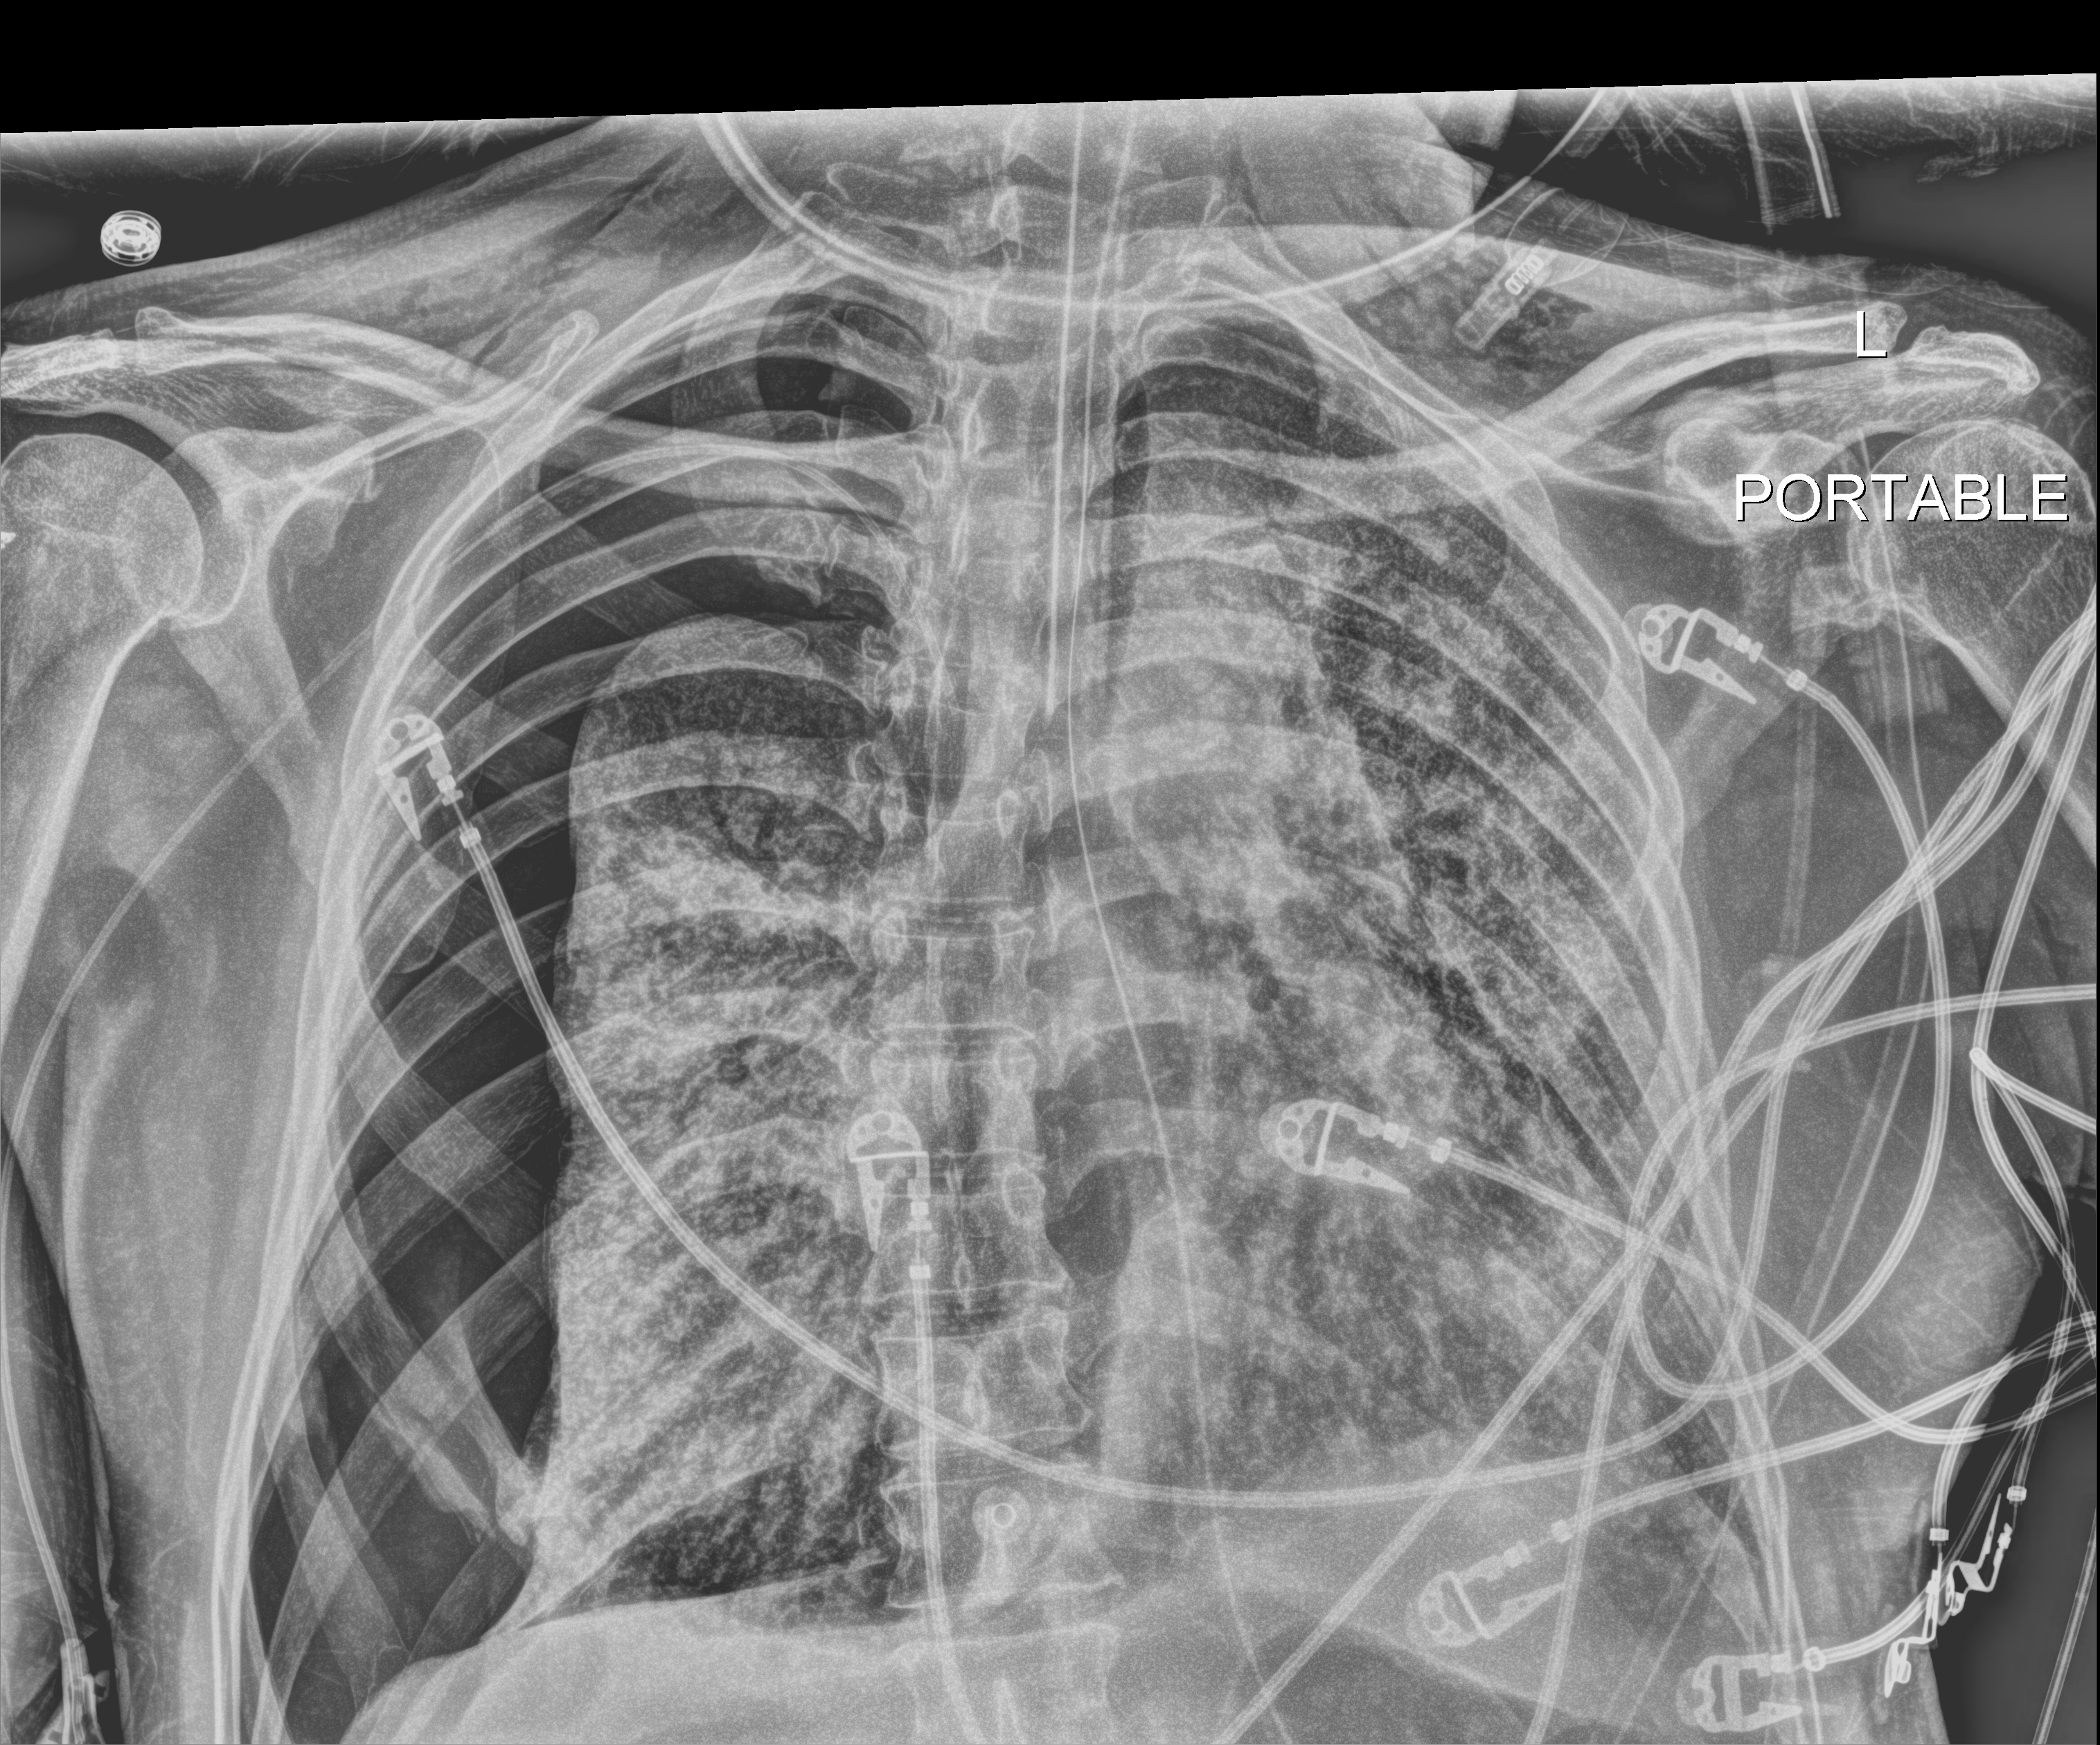
Chest X-ray (portable). Male patient hospitalised with COVID-19, age 60–74 years.
From the hospital-stay record, not from the radiograph (when in the stay this image was taken is not recorded): smoking status (admission record): never; admitted to intensive care during this hospital stay: yes; mechanically ventilated during this hospital stay: yes.